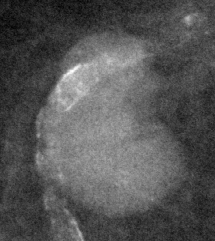
Crop from a digitized film mammogram around one marked abnormality, right breast, MLO view, BI-RADS breast density category 1 (scale 1–4).
Marked abnormality: mass, shape lobulated, margins circumscribed; BI-RADS assessment category 3; subtlety rating 5 on a 1 (subtle) to 5 (obvious) scale; pathology result (as recorded, not read from the image): benign.